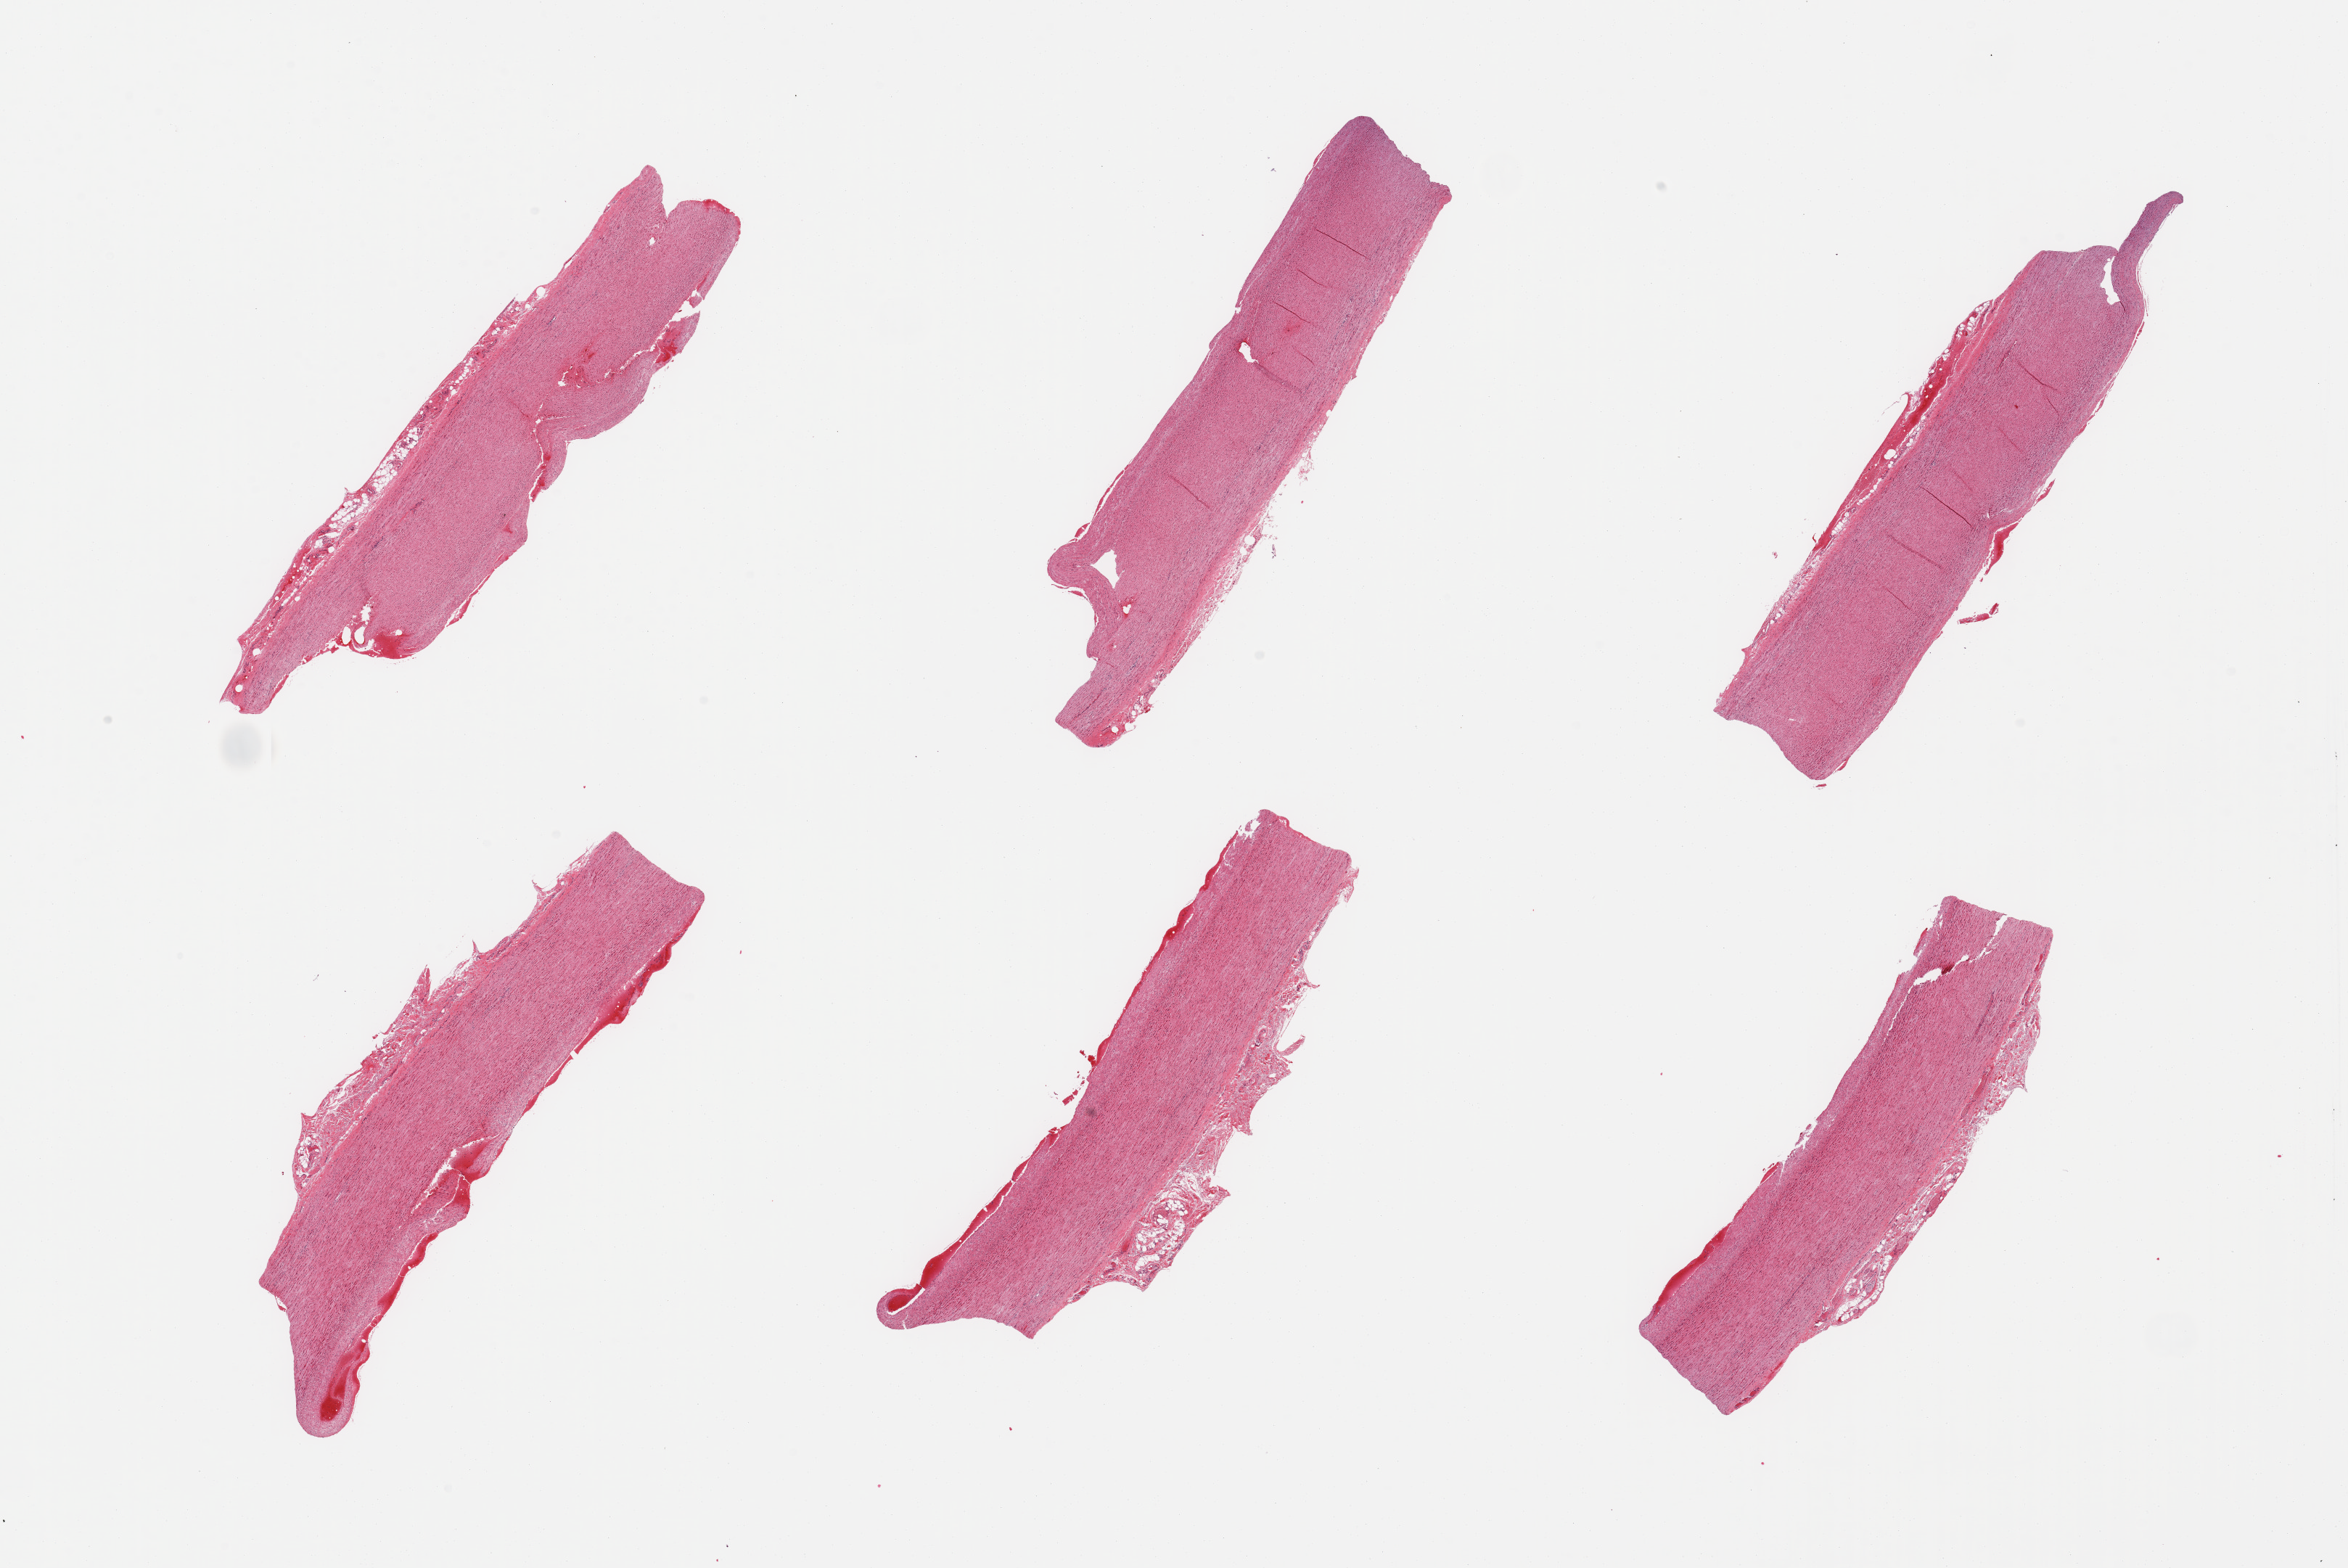
Whole-slide image, hematoxylin and eosin (H&E) stain, low-resolution overview of the scanned area, about 25.6 x 17.1 mm, PAXgene-fixed, paraffin-embedded tissue, section of aorta (target tissue), tissue donor sample. Donor: male.
• reviewer comment on this tissue sample: 6 pieces, minimal atherosis